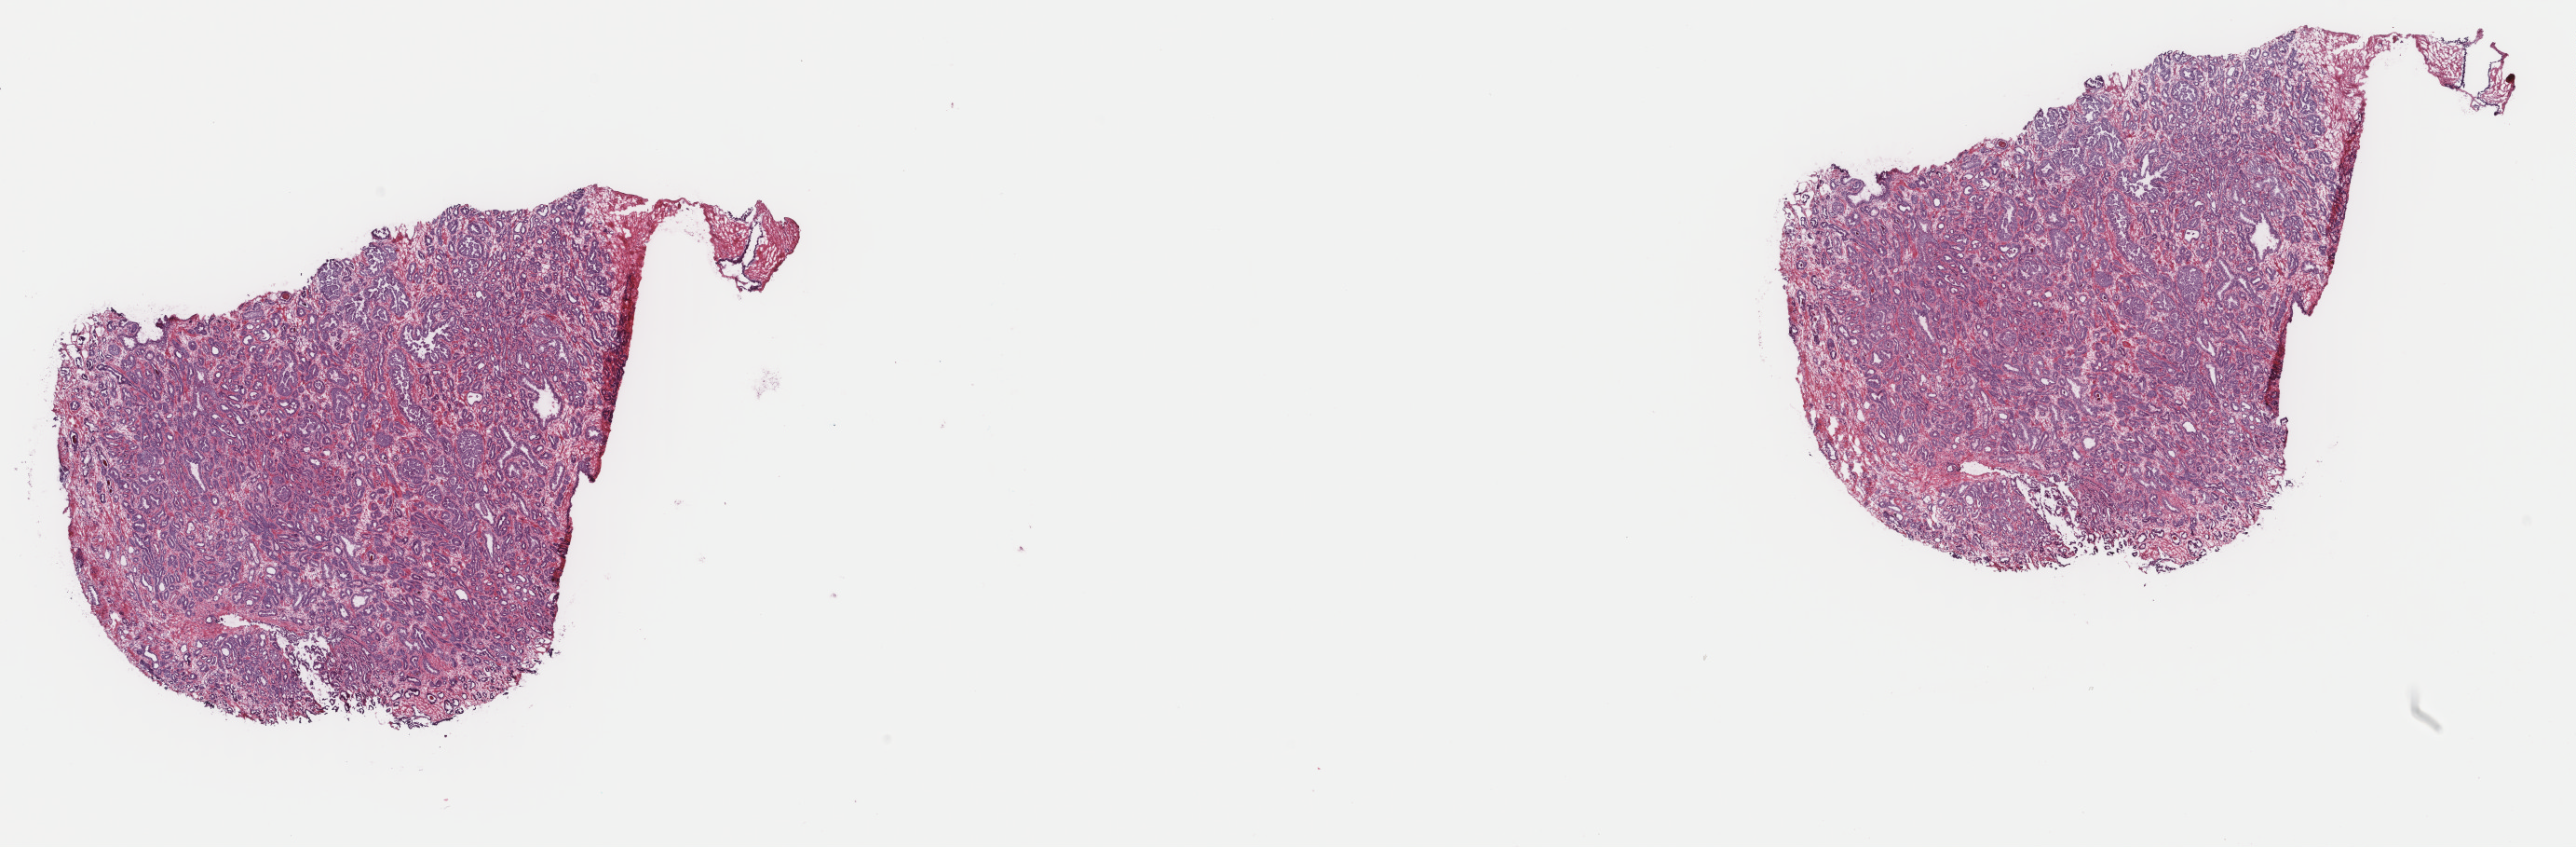
Digitized H&E-stained tissue section (whole slide), low-resolution overview of the scanned area, about 22.0 x 7.2 mm (slide scanned at 40x). Frozen section from the top of the tissue portion. Prostate, primary tumour sample. Male, age 51 years at initial diagnosis. Gleason score: 7 (3+4). Slide review estimates, as recorded: tumour cells 80%, tumour nuclei 80%, normal cells 2%, stromal cells 18%, necrosis 0%. Inflammatory infiltration, as recorded: lymphocyte infiltration 0%, monocyte infiltration 0%, neutrophil infiltration 0%.
- histologic diagnosis: Adenocarcinoma, NOS (prostate gland)